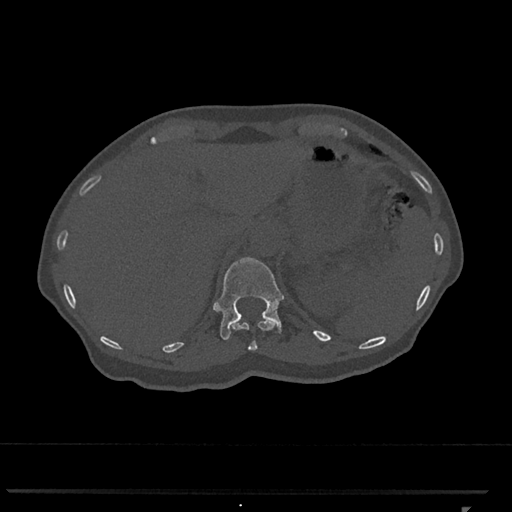
CT including the spine, one axial slice; slice 482 of 793 in the series (ordered by position); reconstruction kernel Br40s/3; 120 kVp; bone window (W 1800 / L 400 HU); 512 × 512 image matrix, field of view 380 × 380 mm. Female patient, age 62 years. From the clinical record (not read from this slice): primary cancer: renal.
Annotated regions visible in this slice (semi-automatic segmentation, software-assisted and operator-edited):
- T11 vertebra: box from (x=232, y=319) to (x=275, y=351) px
- T12 vertebra: (x=214, y=257)–(x=284, y=340)